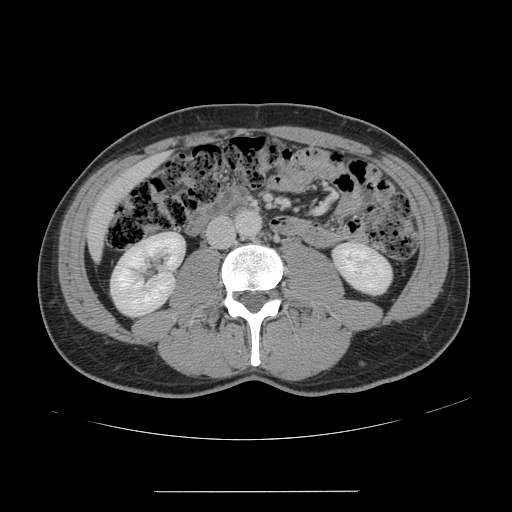
Contrast-enhanced abdominal CT, one axial slice. Position 34 of 178 along the scan axis. Intravenous contrast given. Soft-tissue window (W 400 / L 40 HU). 2.5 mm slice thickness. 512 × 512 image matrix. Male patient, age 53 years. From the clinical record (not read from this slice): diagnosis: colorectal cancer liver metastases, imaged before liver resection; multiple liver metastases: yes; largest metastasis: 2.4 cm; chemotherapy before resection: yes.
Annotated regions visible in this slice (expert manual segmentation):
- liver: bounding box (x1, y1, x2, y2) in pixels: (90, 157, 162, 257)